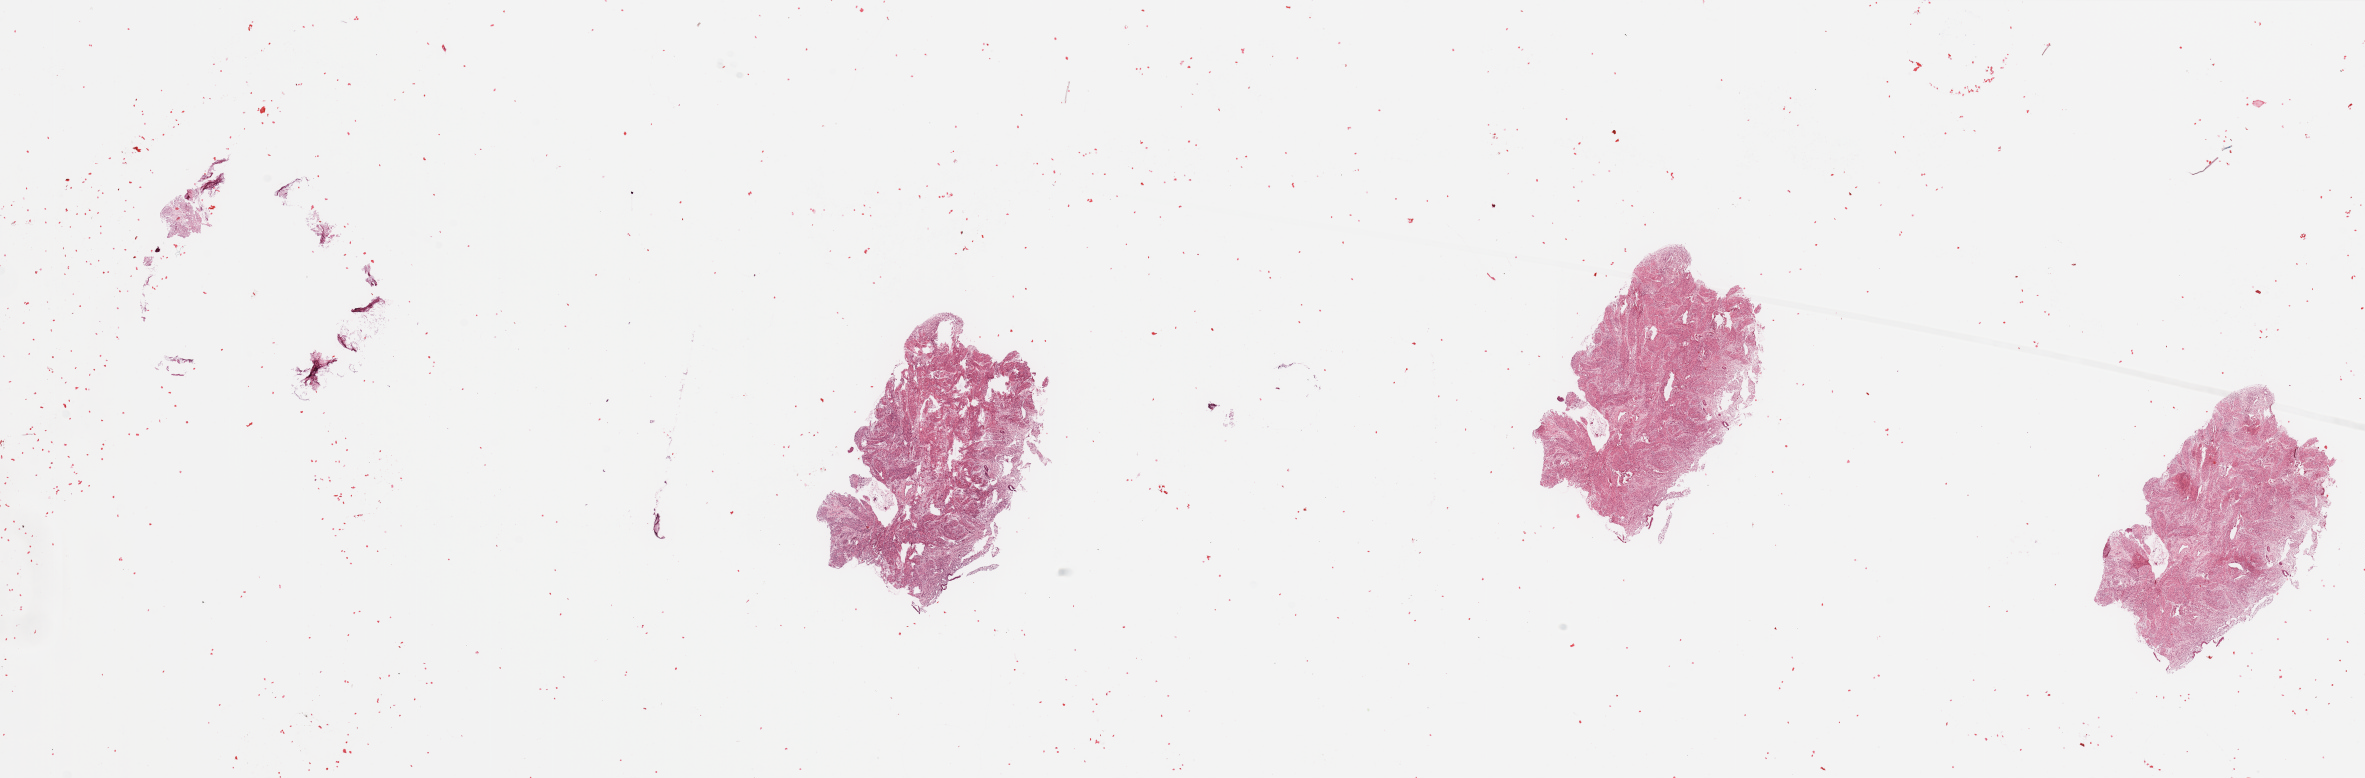
Whole-slide histology image, H&E-stained, shown as a low-resolution overview of the whole scanned area (about 37.4 x 12.3 mm); uterus, normal (non-tumour) tissue. 80-year-old female patient.
This section: normal (non-tumour) tissue from the same patient. Patient diagnosis: Endometrioid adenocarcinoma, NOS.